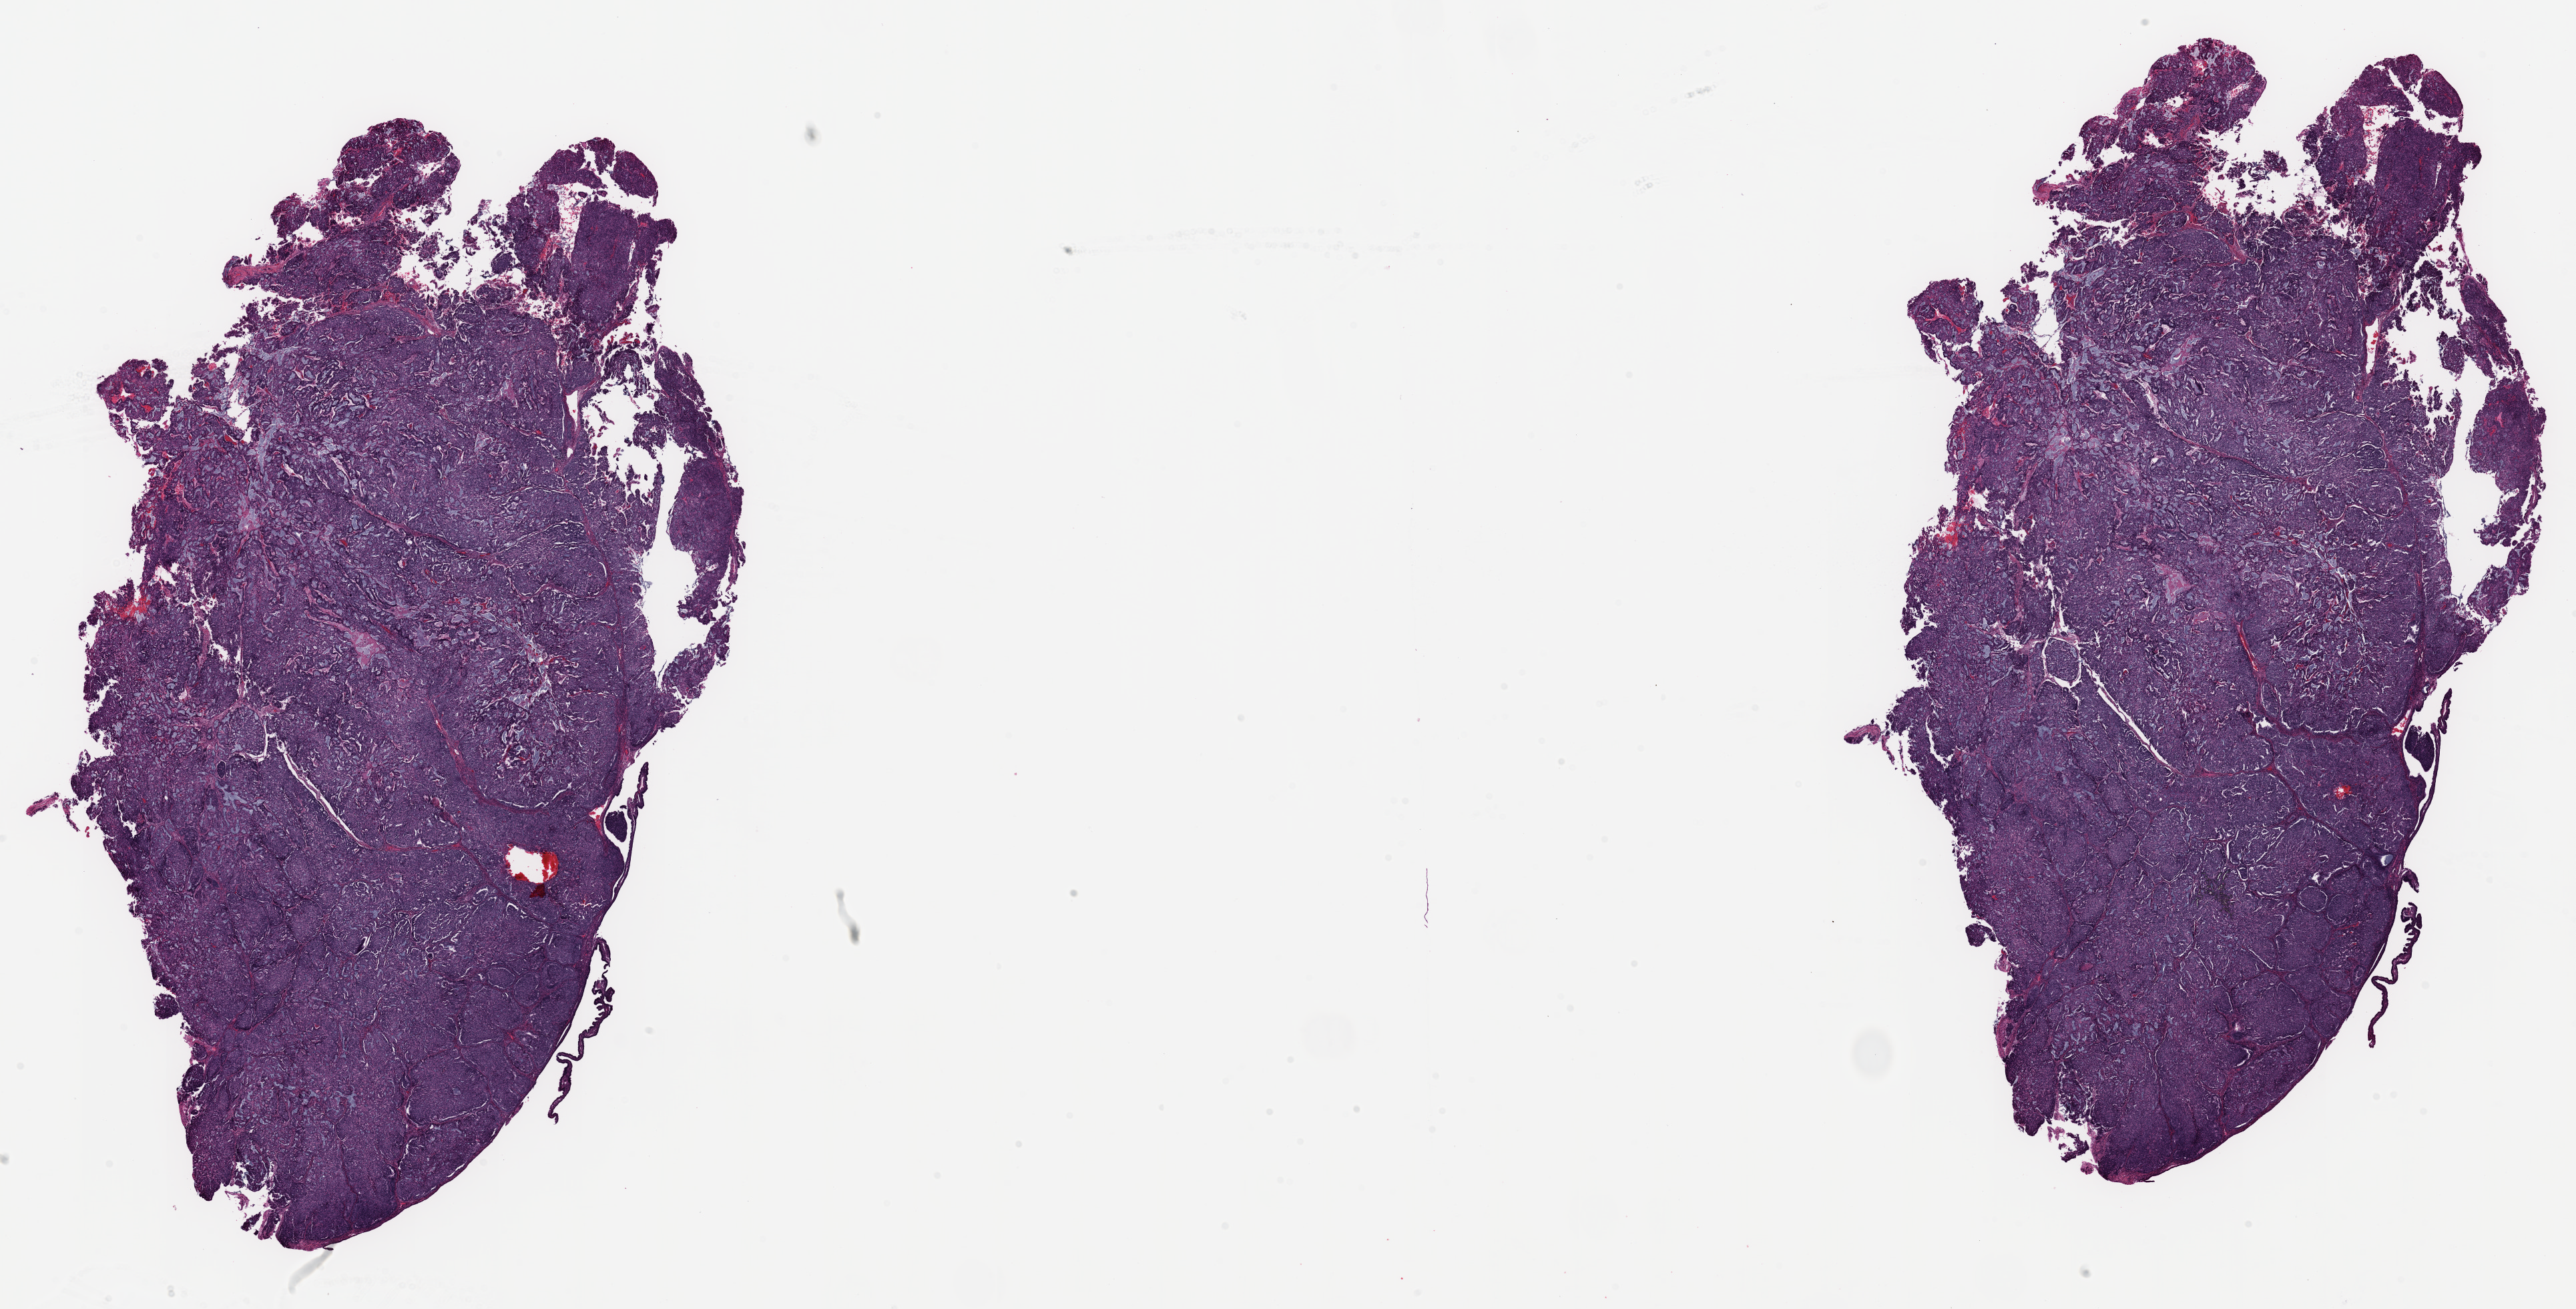
Whole-slide histology image, H&E-stained — a low-resolution overview of the entire scanned area, about 30.5 x 15.5 mm (acquisition: 20x scan). Formalin-fixed paraffin-embedded (FFPE) diagnostic section. Sample: primary tumour, uterus. Patient: female, age at initial diagnosis 60 years. Histologic grade: G3 (poorly differentiated).
• FIGO stage: IIIA
• histologic diagnosis: Serous cystadenocarcinoma, NOS (endometrium)